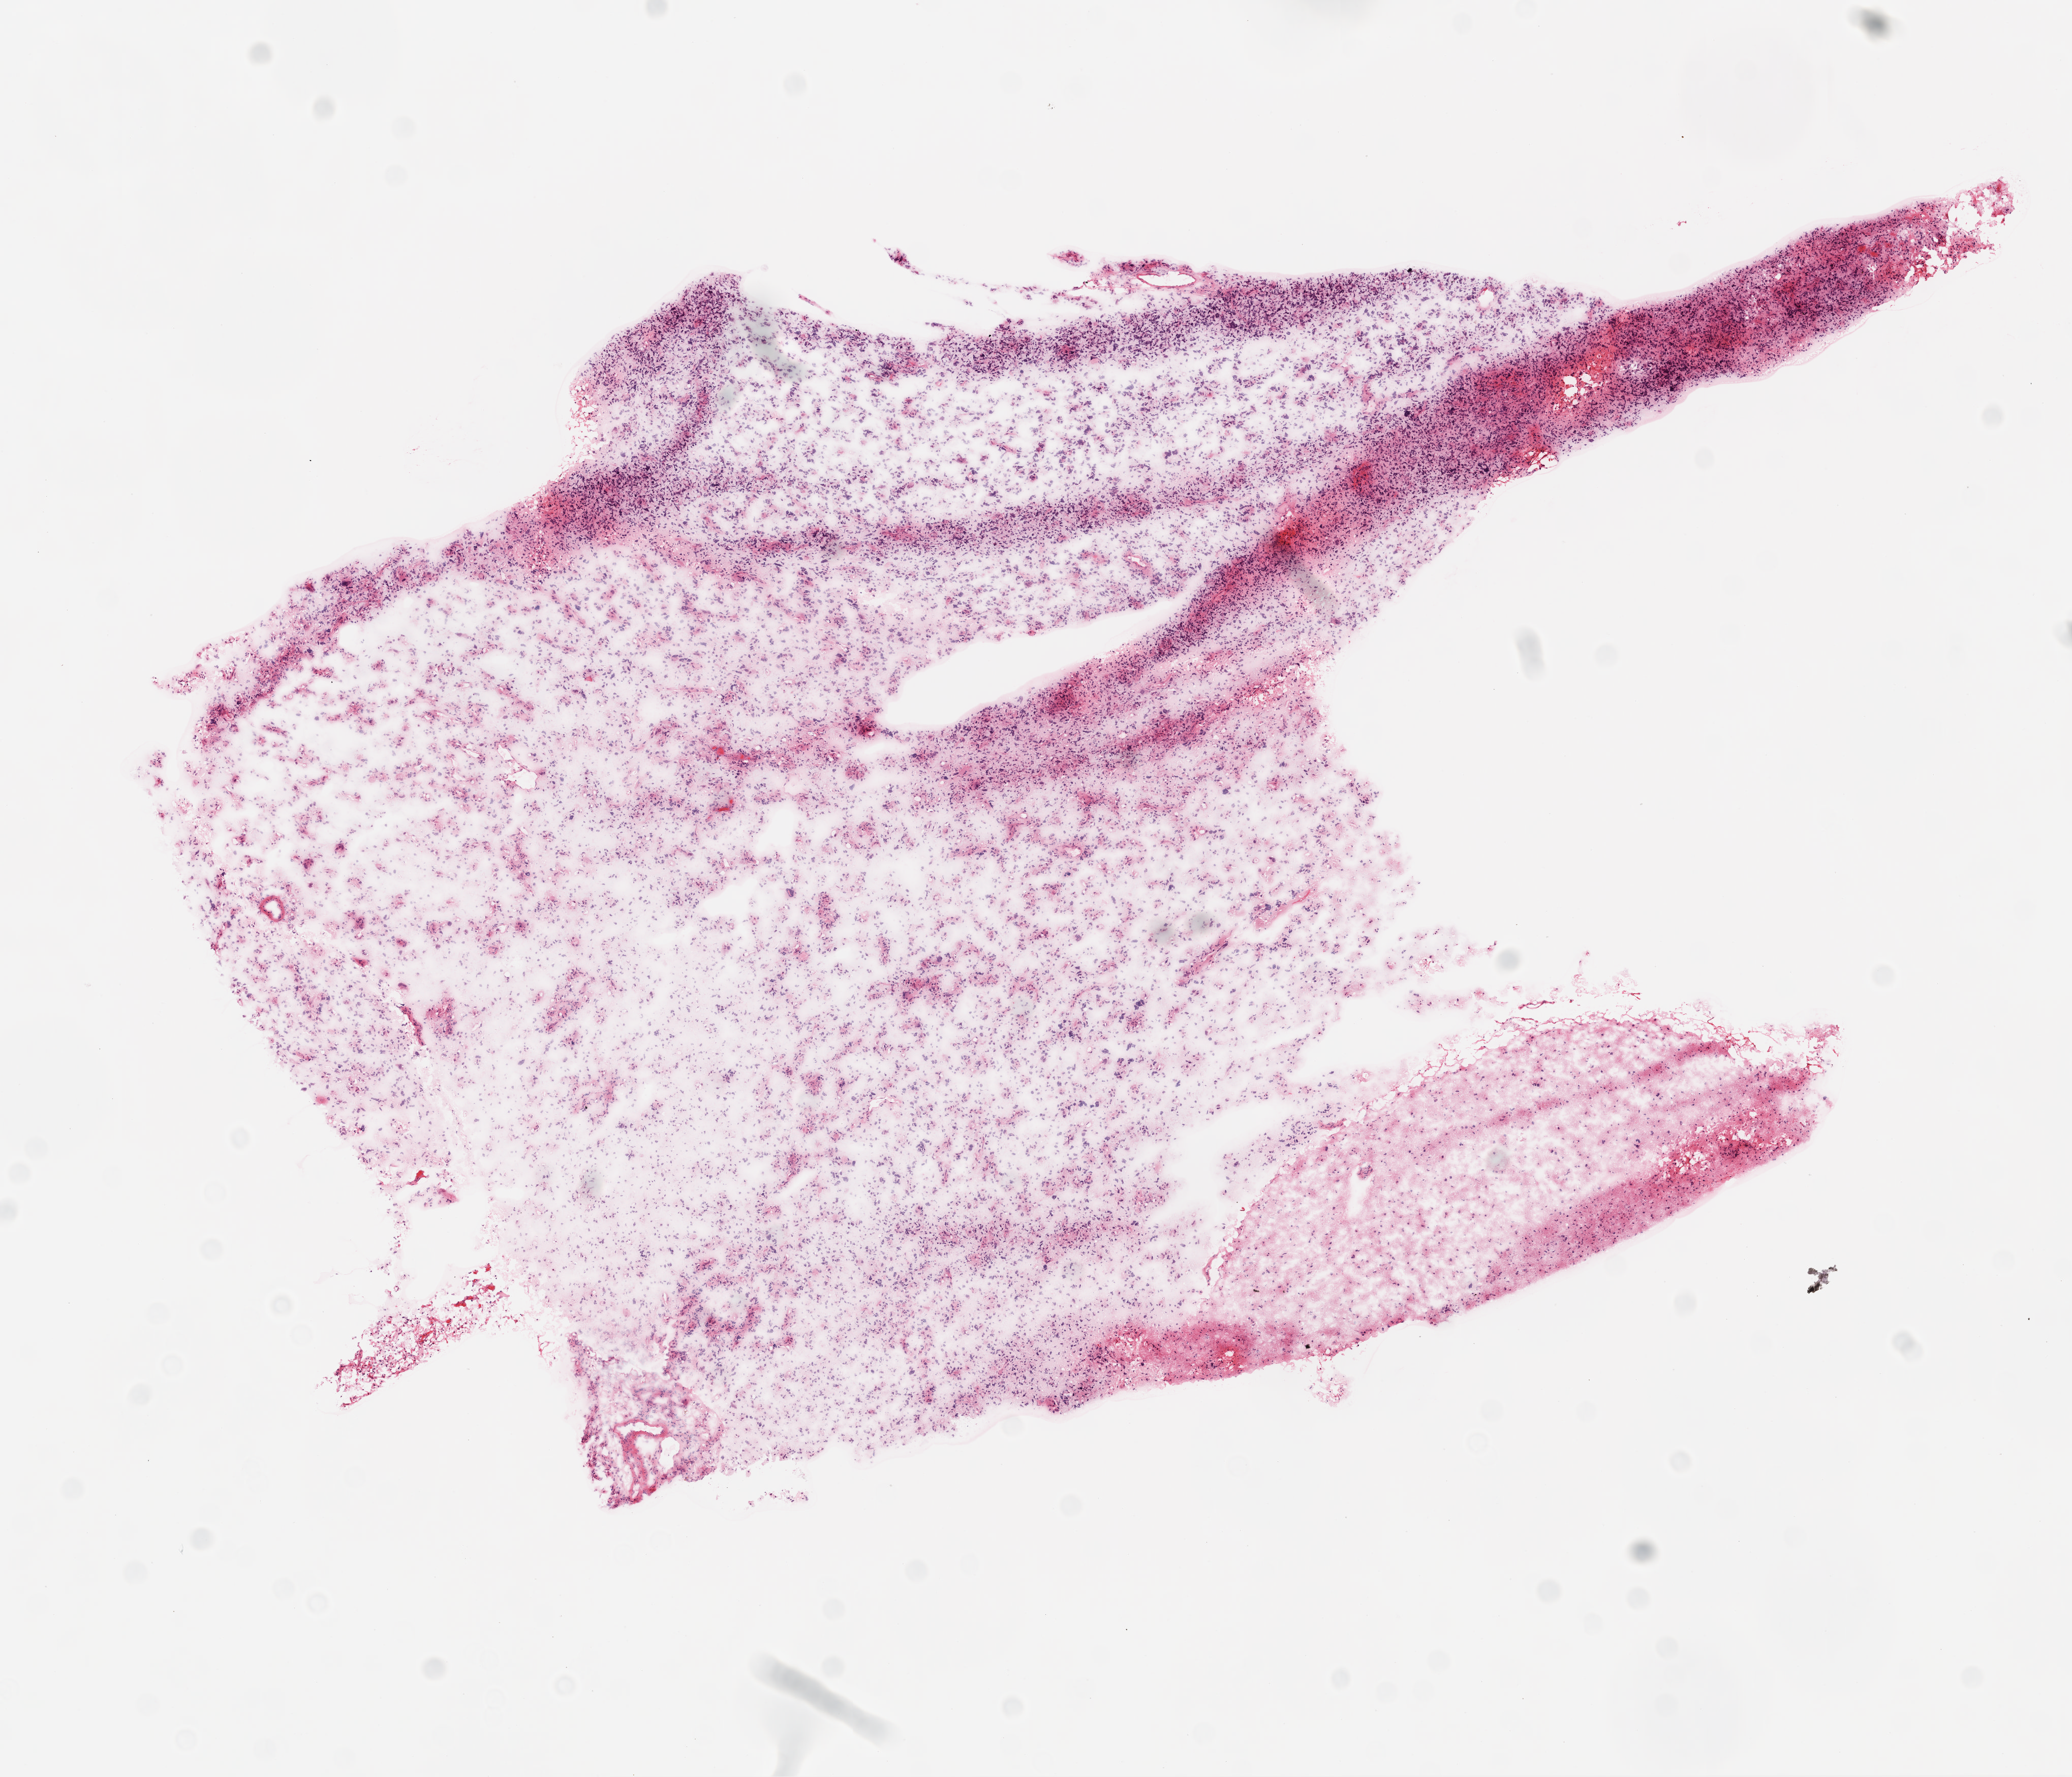
Hematoxylin and eosin (H&E) stained whole-slide image, low-resolution overview of the scanned area, about 8.2 x 7.0 mm (acquisition: 20x scan). Frozen section. Primary tumour sample from the brain. Patient: male, age at initial diagnosis 32 years. Pathologist review of this section (percent, as recorded): tumour cells 85%, tumour nuclei 90%, normal cells 0%, stromal cells 0%, necrosis 15%.
Histologic diagnosis: Glioblastoma.